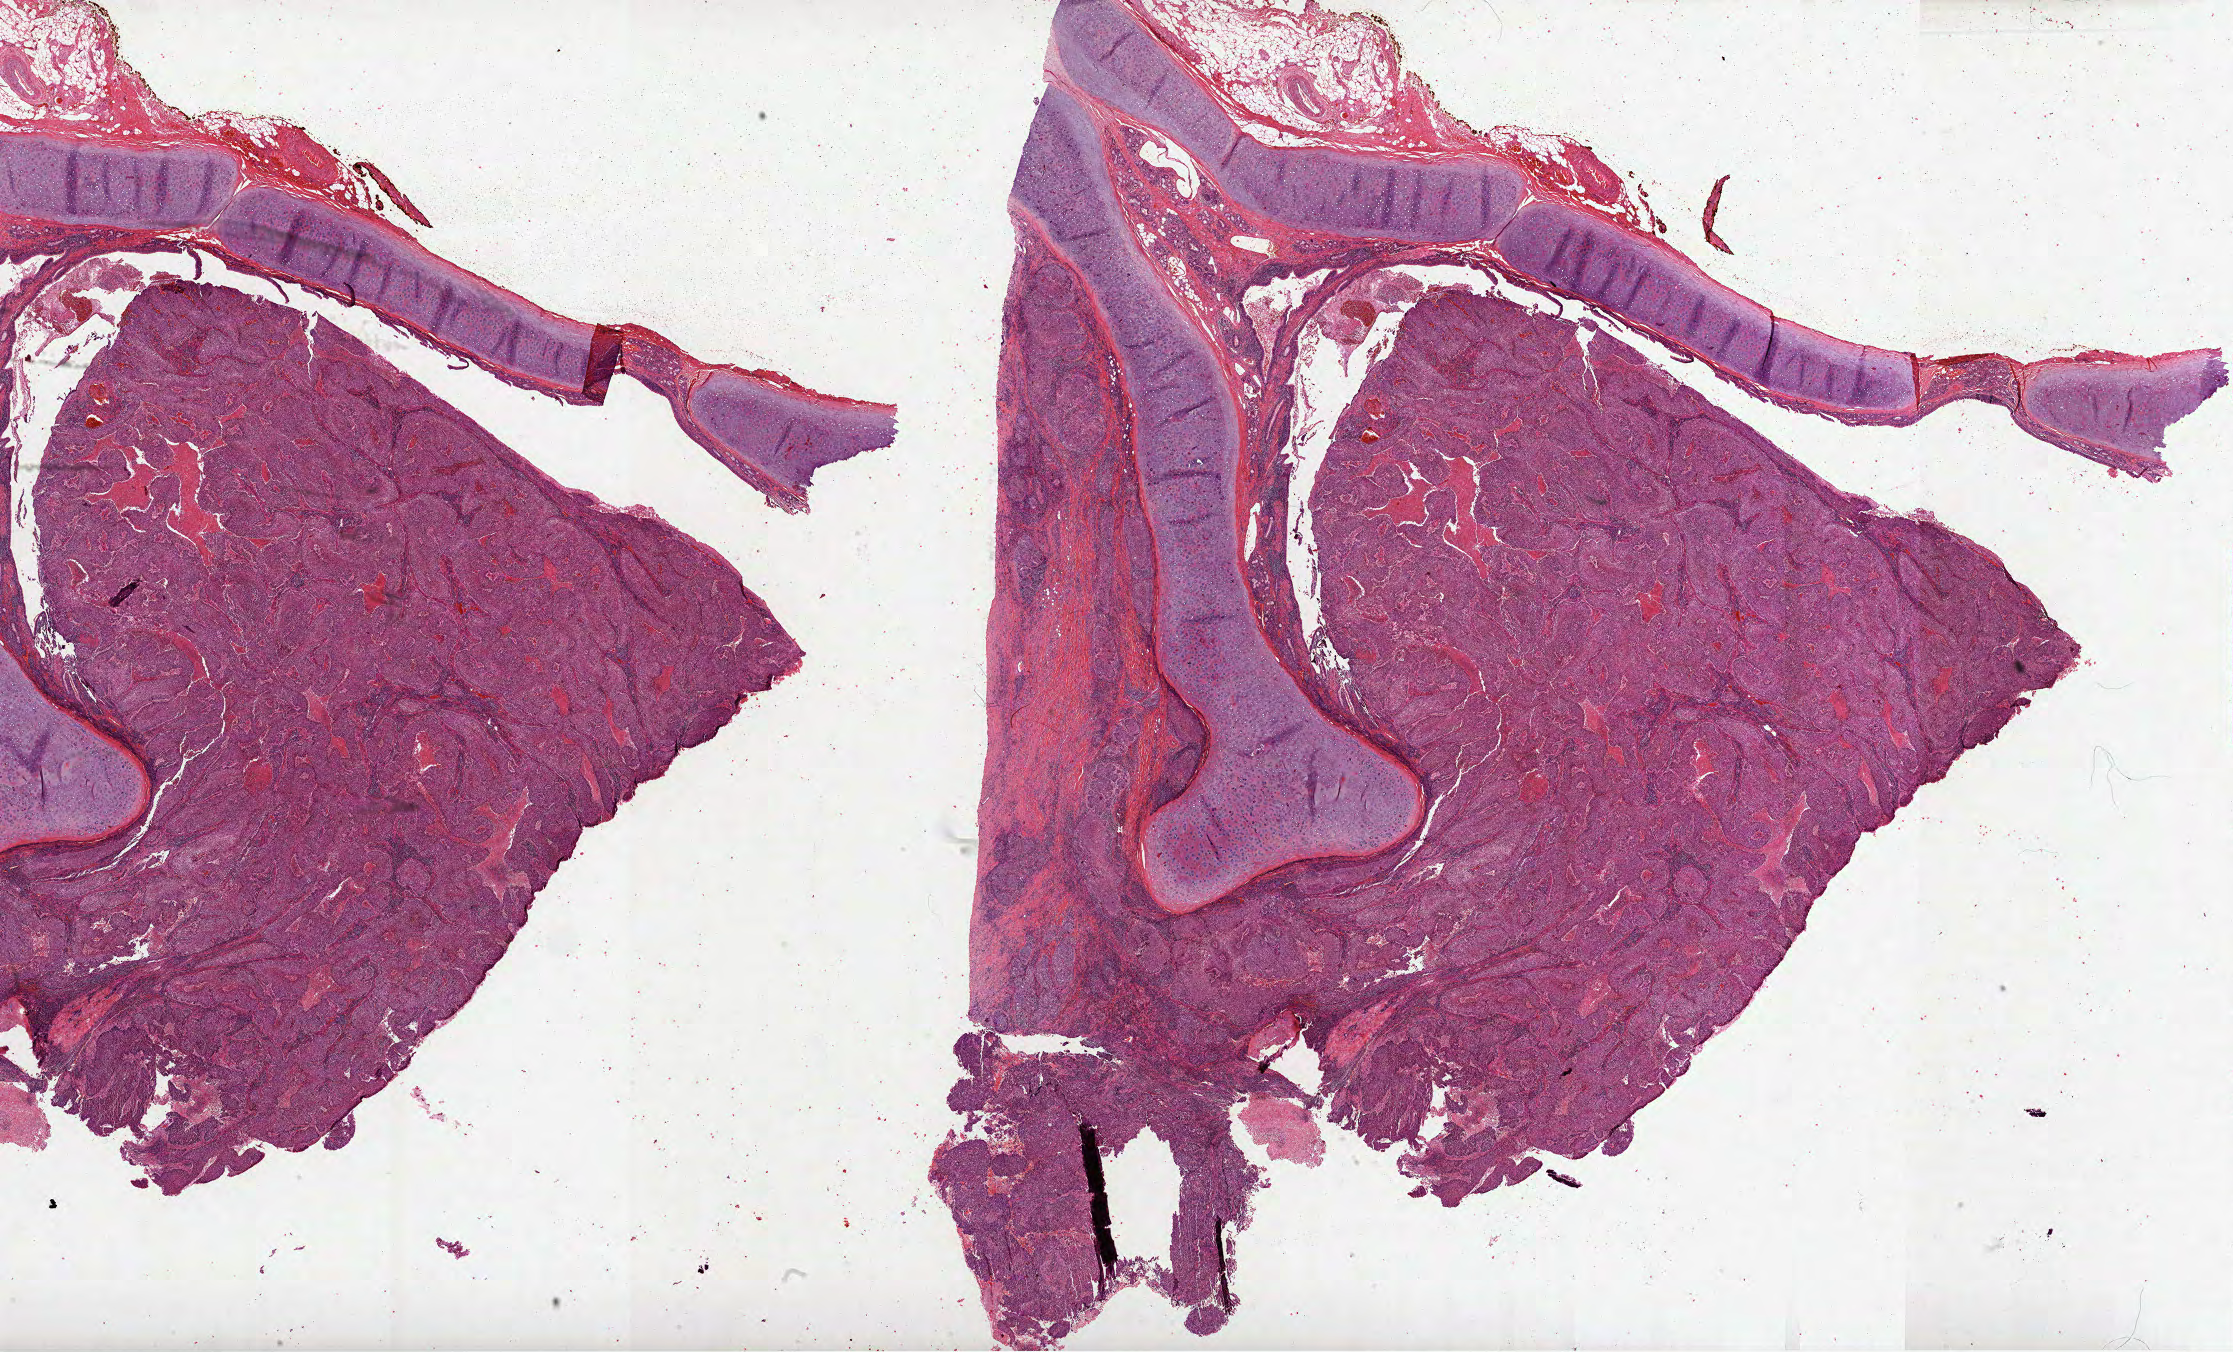
Digitized H&E tissue section (whole slide) — shown as a low-resolution overview of the whole scanned area (about 36.0 x 21.8 mm, slide scanned at 40x), FFPE section, lung, primary tumour sample. Patient: male, age at initial diagnosis 70 years.
Pathologic diagnosis: Squamous cell carcinoma, NOS. TNM: T2 N1 M0. AJCC pathologic stage: IIB.